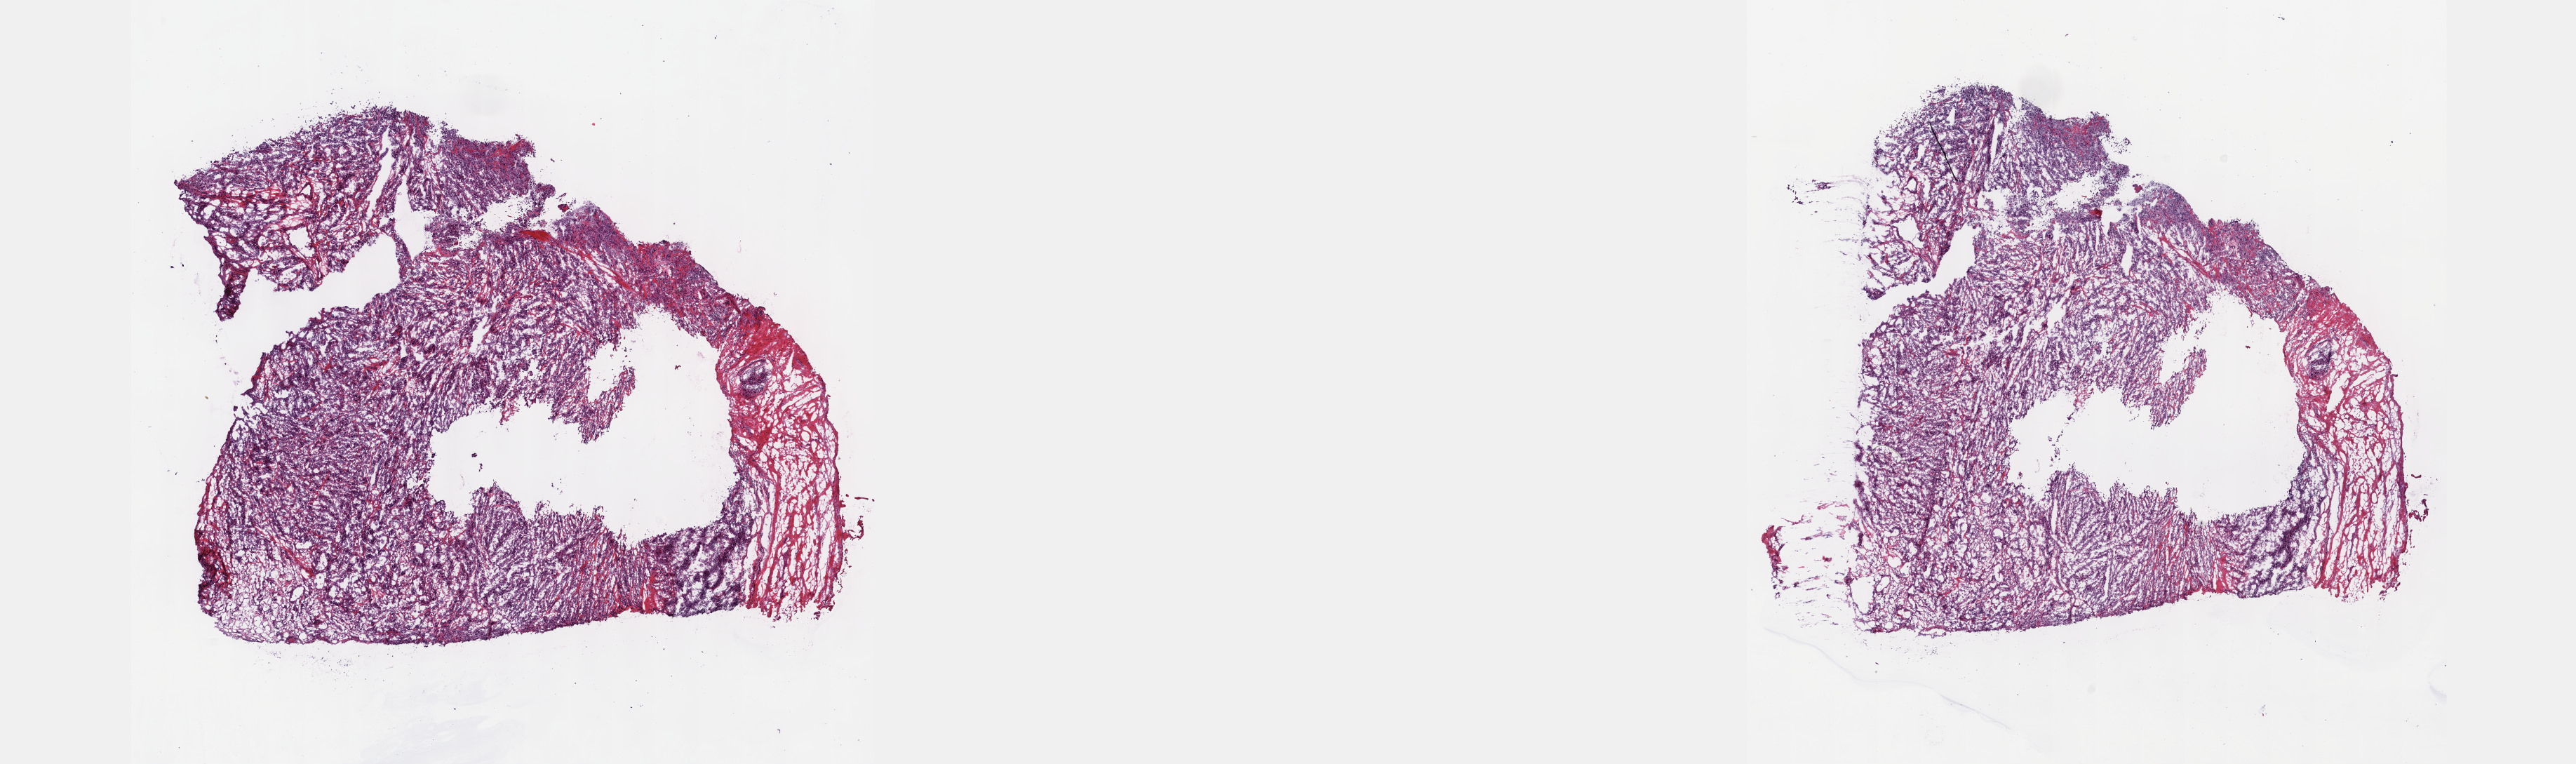
Whole-slide histology image, H&E-stained, whole scanned area (about 29.7 x 8.8 mm, from a 40x scan) shown as a low-resolution overview. FFPE section. Breast, primary tumour sample. Patient: female, age at initial diagnosis 29 years. Slide review estimates, as recorded: tumour cells 63%, tumour nuclei 80%, normal cells 2%, stromal cells 30%, necrosis 5%. Inflammatory infiltration, as recorded: lymphocyte infiltration 14%, monocyte infiltration 2%, neutrophil infiltration 2%.
Laterality: left. Histologic diagnosis: Infiltrating duct carcinoma, NOS. AJCC pathologic stage: IIIB (7th edition). TNM: T4b N2 M0.